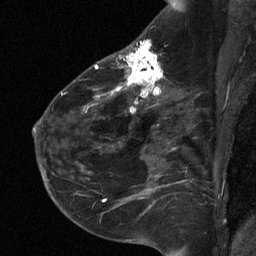
Breast MRI (dynamic contrast-enhanced), one sagittal slice; position 41 of 64 along the scan axis; dynamic contrast-enhanced study with each time point stored as its own series, time point 2 of 3 at this slice position (early post-contrast, ordered by acquisition time); 1.5 T; TE 4.8 ms, TR 27 ms; 256 × 256 image matrix, field of view 180 × 180 mm. Patient: female, 51 years. From the clinical record (not read from this slice): setting: breast cancer imaged before/during neoadjuvant chemotherapy; receptor status: HR-positive, HER2-negative.
Annotated regions visible in this slice (semi-automatically segmented with operator editing):
- analysis volume of interest (the breast-tissue region the enhancement analysis was run in; not a lesion): bounding box <72,34,182,118> (left, top, right, bottom; pixels)
- tumour enhancement mask (voxels above the 90 % enhancement threshold inside the analysis volume of interest): <95,39,163,114>